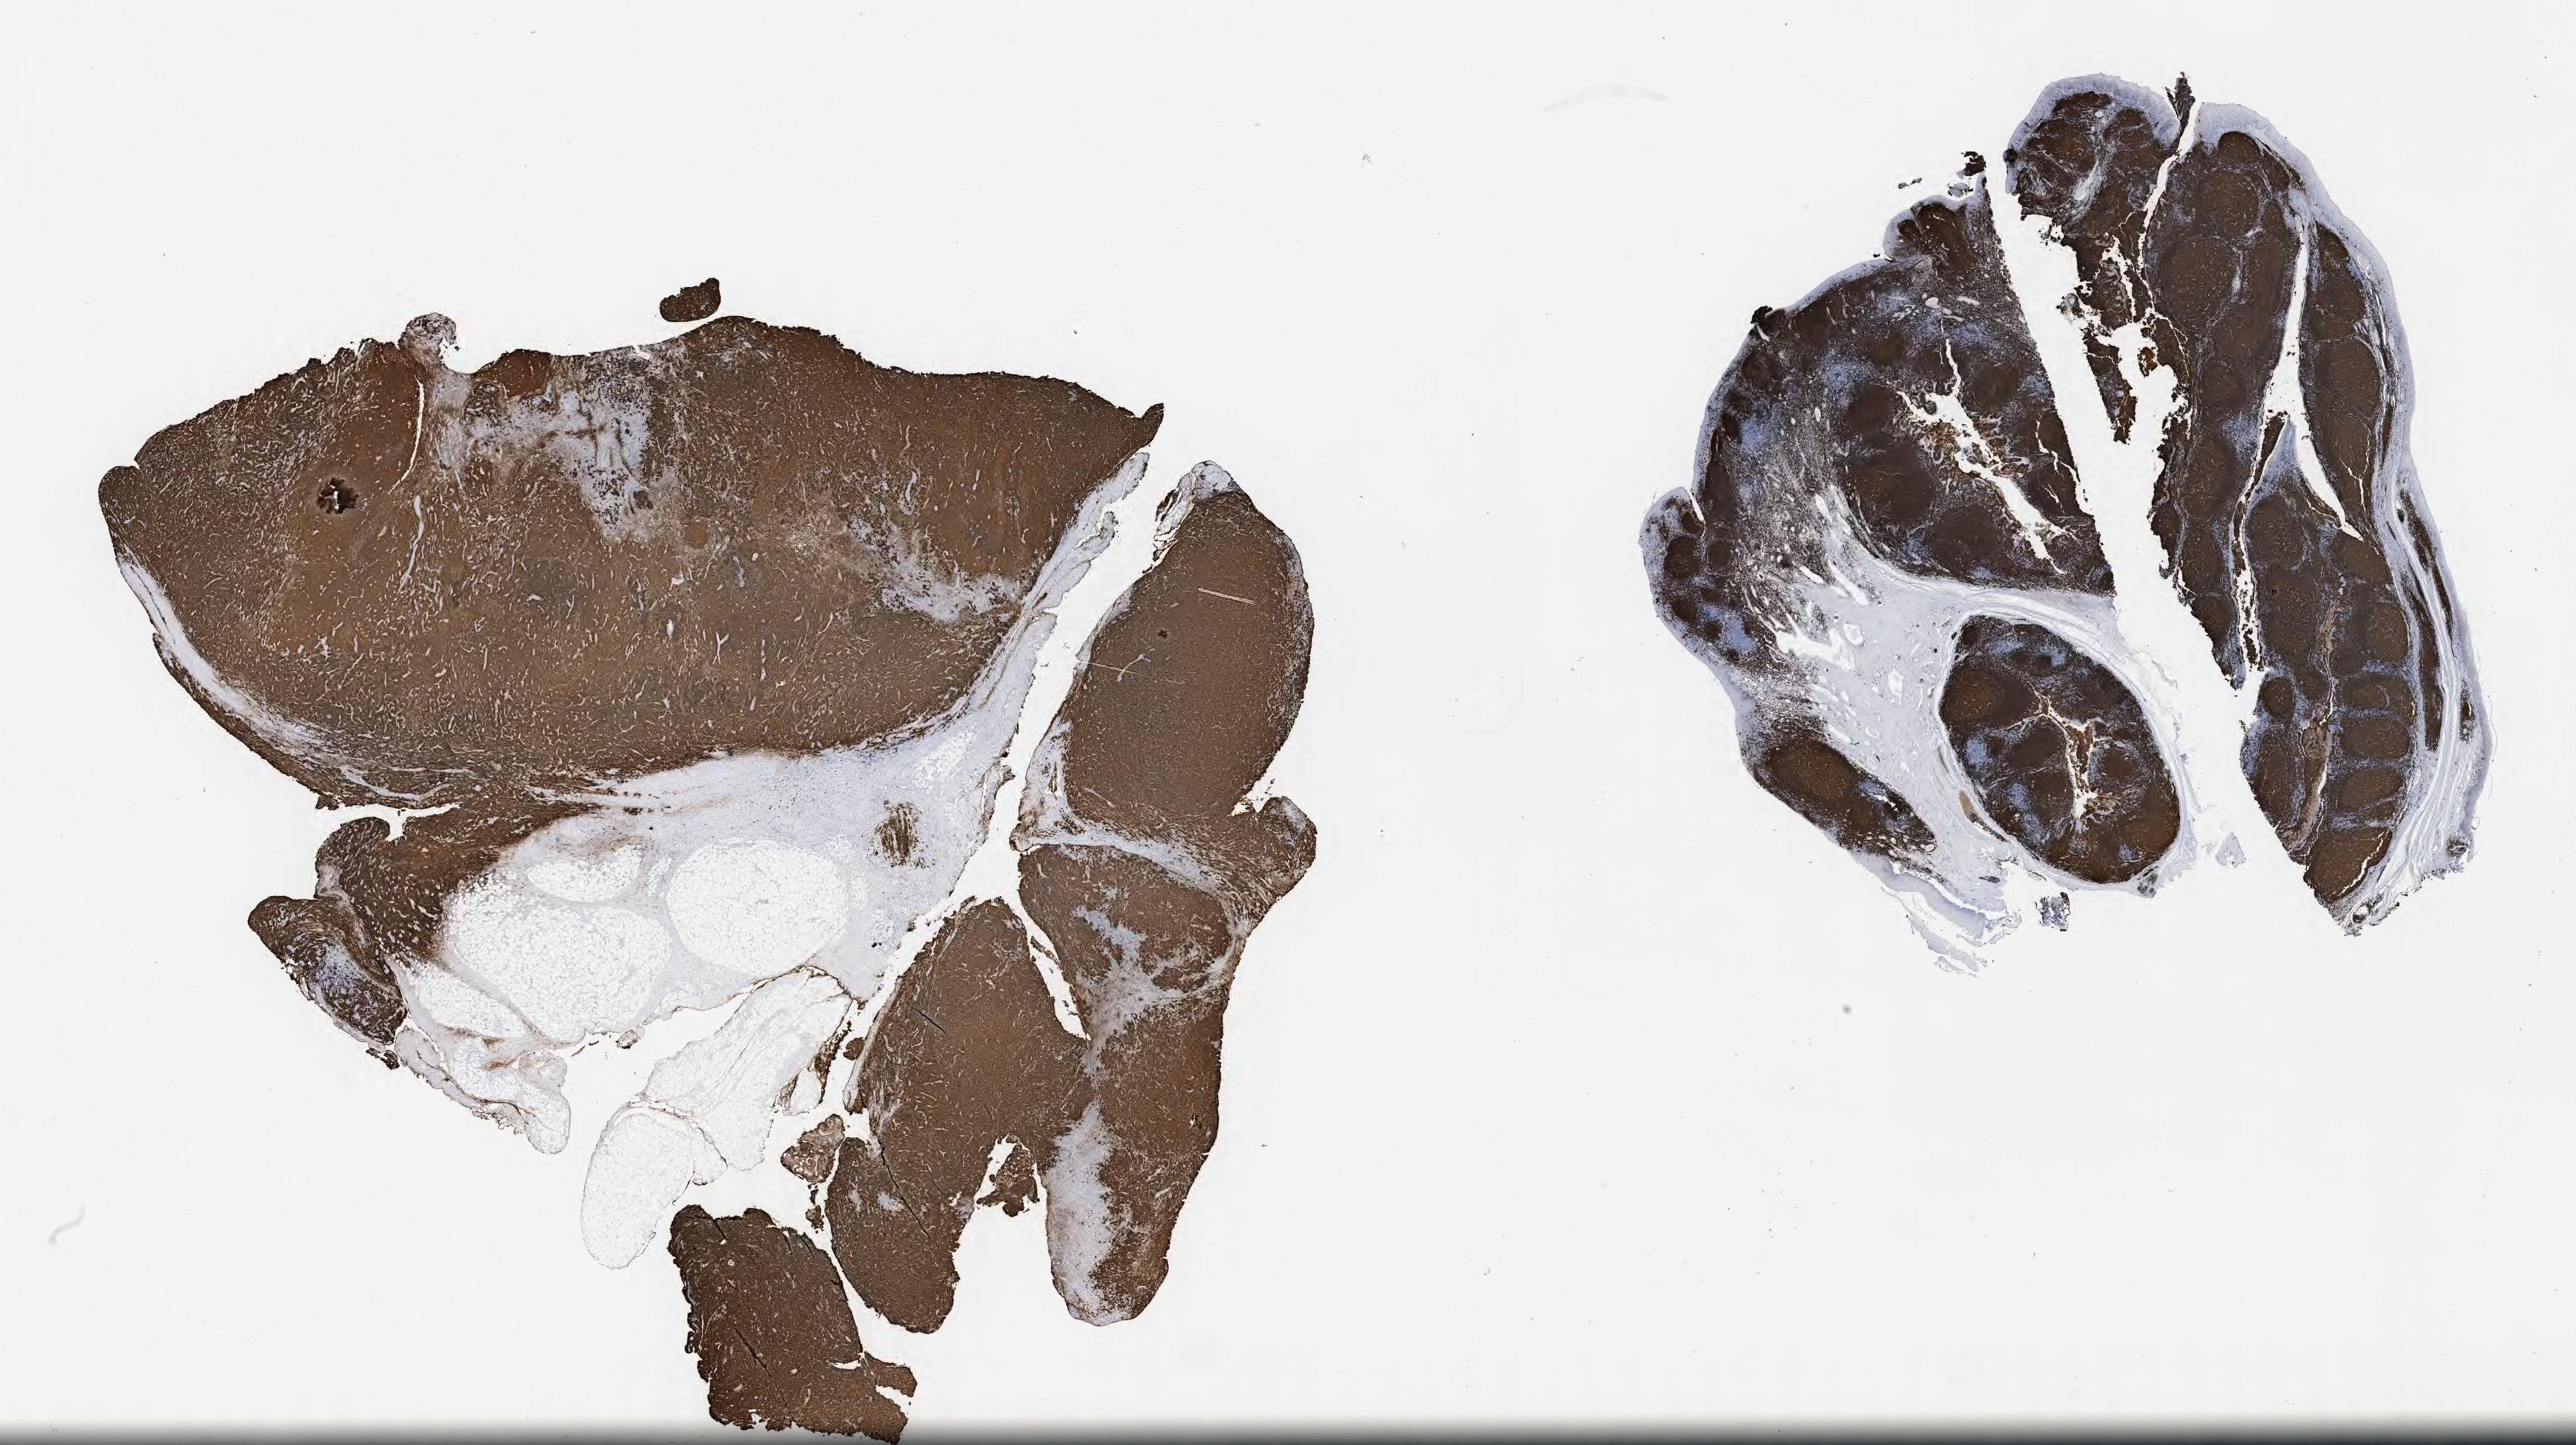
Immunohistochemistry (IHC) whole-slide image stained for CD20 — low-resolution overview of the scanned area, about 32.2 x 18.1 mm; specimen: tumor tissue. Patient: female, age 46 years.
Histologic diagnosis: Diffuse large B-cell lymphoma, NOS.